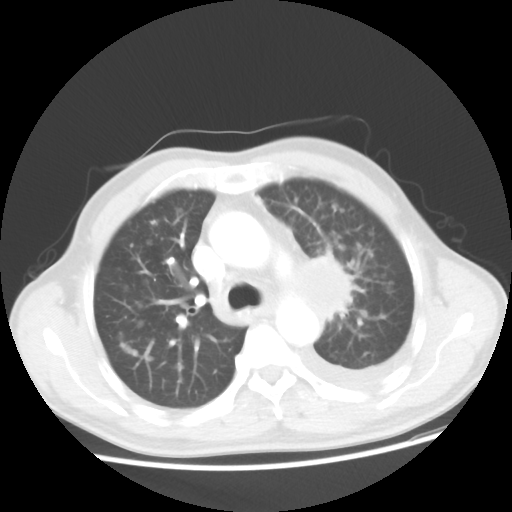
Chest CT, one axial slice. Slice 32 of 48 in the series (ordered by position). Reconstruction kernel STANDARD. 100 kVp. Lung window (W 1500 / L -600 HU). 5 mm slice thickness. 512 × 512 image matrix, field of view 362 × 362 mm. Male patient, age 55 years. From the clinical record (not read from this slice): clinical TNM (as recorded): T2 N3 M1a; histopathological grade: G3.
Structures marked on this image (bounding box drawn by a radiologist):
- lung tumour (recorded histology: squamous cell carcinoma): bounding box <304,248,352,329> (left, top, right, bottom; pixels)